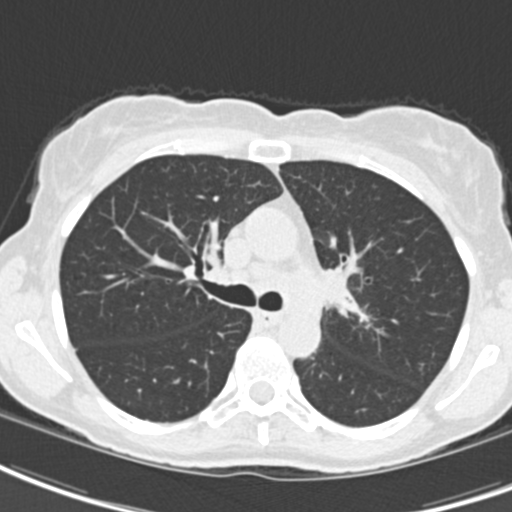
Chest CT (low-dose screening protocol), one axial image. Baseline screening round. Lung window (W 1500 / L -600 HU). 2 mm slice thickness. Female participant, aged 62 years at enrolment. Current smoker at enrolment.
Lesion marked by an expert reader, bounding box (x1, y1, x2, y2) in pixels: (293, 251, 367, 335). The exam's reader record, not a measurement of the box and not confirmed to be the same lesion: non-calcified nodule or mass ≥4 mm, right upper lobe, 24 × 20 mm, smooth margins, ground glass attenuation. Note: the box lies in the patient's left hemithorax on this image, whereas the reader's record names the right lung; they may be different findings.